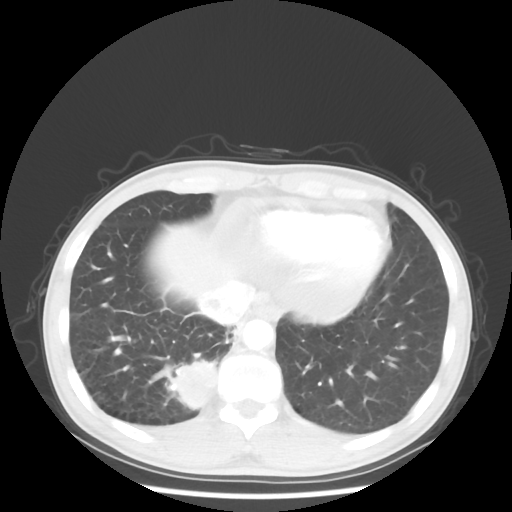
Chest CT, one axial slice. Position 11 of 58 along the scan axis. Reconstruction kernel STANDARD. 100 kVp. Lung window (W 1500 / L -600 HU). 5 mm slice thickness. 512 × 512 image matrix. Male patient, age 56 years. Case-level facts recorded for this patient, not image findings: clinical TNM (as recorded): T2 N1 M1; histopathological grade: G1.
Structures marked on this image (rectangle marked by the reading radiologist):
- lung tumour (recorded histology: adenocarcinoma): box from (x=163, y=354) to (x=218, y=409) px